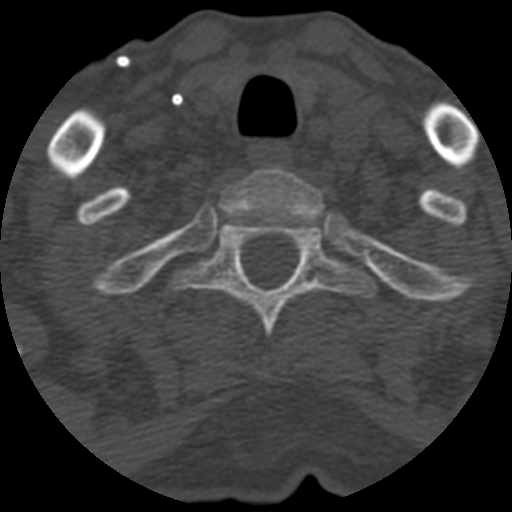
CT including the spine, one axial slice. Position 508 of 708 along the scan axis. 120 kVp. One of 3 acquisitions stored at this slice position. Bone window (W 1800 / L 400 HU). 1.25 mm slice thickness. 512 × 512 image matrix, field of view 160 × 160 mm. Patient age 55 years. From the clinical record (not read from this slice): primary cancer: colon.
Outlined on this slice (semi-automatic segmentation, software-assisted and operator-edited):
- T1 vertebra: bounding box <221,168,322,223> (left, top, right, bottom; pixels)
- T2 vertebra: <171,221,373,337>